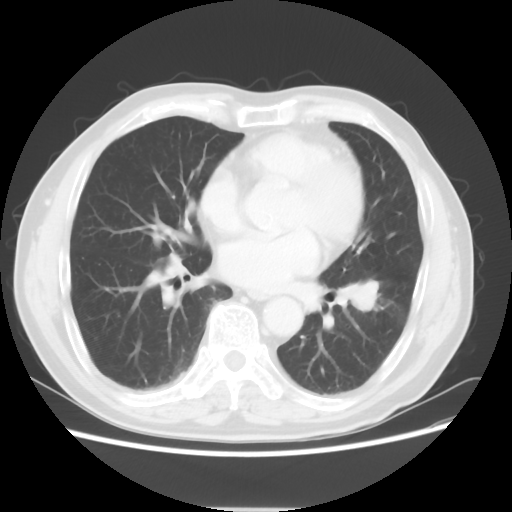
Chest CT, one axial slice; slice 26 of 64 in the series (ordered by position); 120 kVp; lung window (W 1500 / L -600 HU); 5 mm slice thickness; 512 × 512 image matrix, field of view 366 × 366 mm. Male patient, age 71 years. Case-level facts recorded for this patient, not image findings: clinical TNM (as recorded): T1c N1 M0.
Outlined on this slice (bounding box drawn by a radiologist):
- lung tumour (recorded histology: adenocarcinoma): bounding box (x1, y1, x2, y2) in pixels: (342, 269, 389, 322)